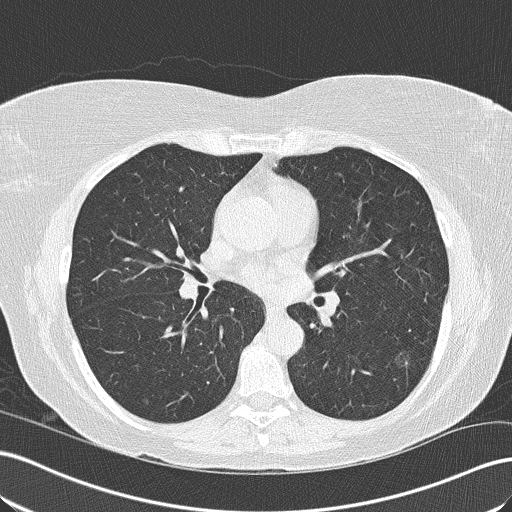
Axial slice from a low-dose chest CT screening exam. Second screening round (one year after baseline). Lung window (W 1500 / L -600 HU). Lung (sharp) reconstruction kernel (B50f). 120 kVp. Female, age 57 years at enrolment. Current smoker at enrolment.
• Expert reader's lesion annotation, bounding box (x1, y1, x2, y2) in pixels: (378, 340, 430, 386).
• The screening reader recorded 6 non-calcified nodules or masses ≥4 mm on this exam (left lower lobe, right upper lobe, right upper lobe, right upper lobe, right lower lobe, right upper lobe); which of them this box marks is not recorded.
• Official screen result: positive, no significant change: stable abnormalities potentially related to lung cancer, unchanged since the prior screening exam.
• Lung cancer was diagnosed 482 days after this screen: bronchiolo-alveolar adenocarcinoma, NOS, left lower lobe, well differentiated (G1), stage IA (AJCC 6th edition), 16 mm at pathology.